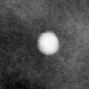
Cropped region of a digitized screen-film mammogram centred on a radiologist-marked abnormality, right breast, CC view.
Calcifications, morphology round and regular / lucent center; BI-RADS assessment category 2; benign without callback (not worked up further).